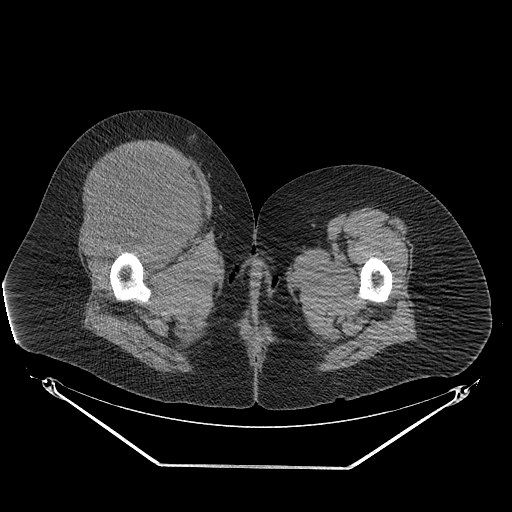
CT of an extremity soft-tissue mass (from a PET/CT study), one axial slice. Position 48 of 267 along the scan axis. Reconstruction kernel STANDARD. 140 kVp. Soft-tissue window (W 400 / L 40 HU). 3.75 mm slice thickness. 512 × 512 image matrix, field of view 500 × 500 mm. Female patient. From the clinical record (not read from this slice): histological type: malignant solitary fibrous tumor; grade: intermediate; site of the primary tumour: right thigh.
Outlined on this slice (expert contour drawn on MRI and transferred to this co-registered scan by the dataset authors):
- gross tumour volume including surrounding oedema: bounding box <75,148,204,245> (left, top, right, bottom; pixels)
- gross tumour volume (mass): <80,148,202,243>